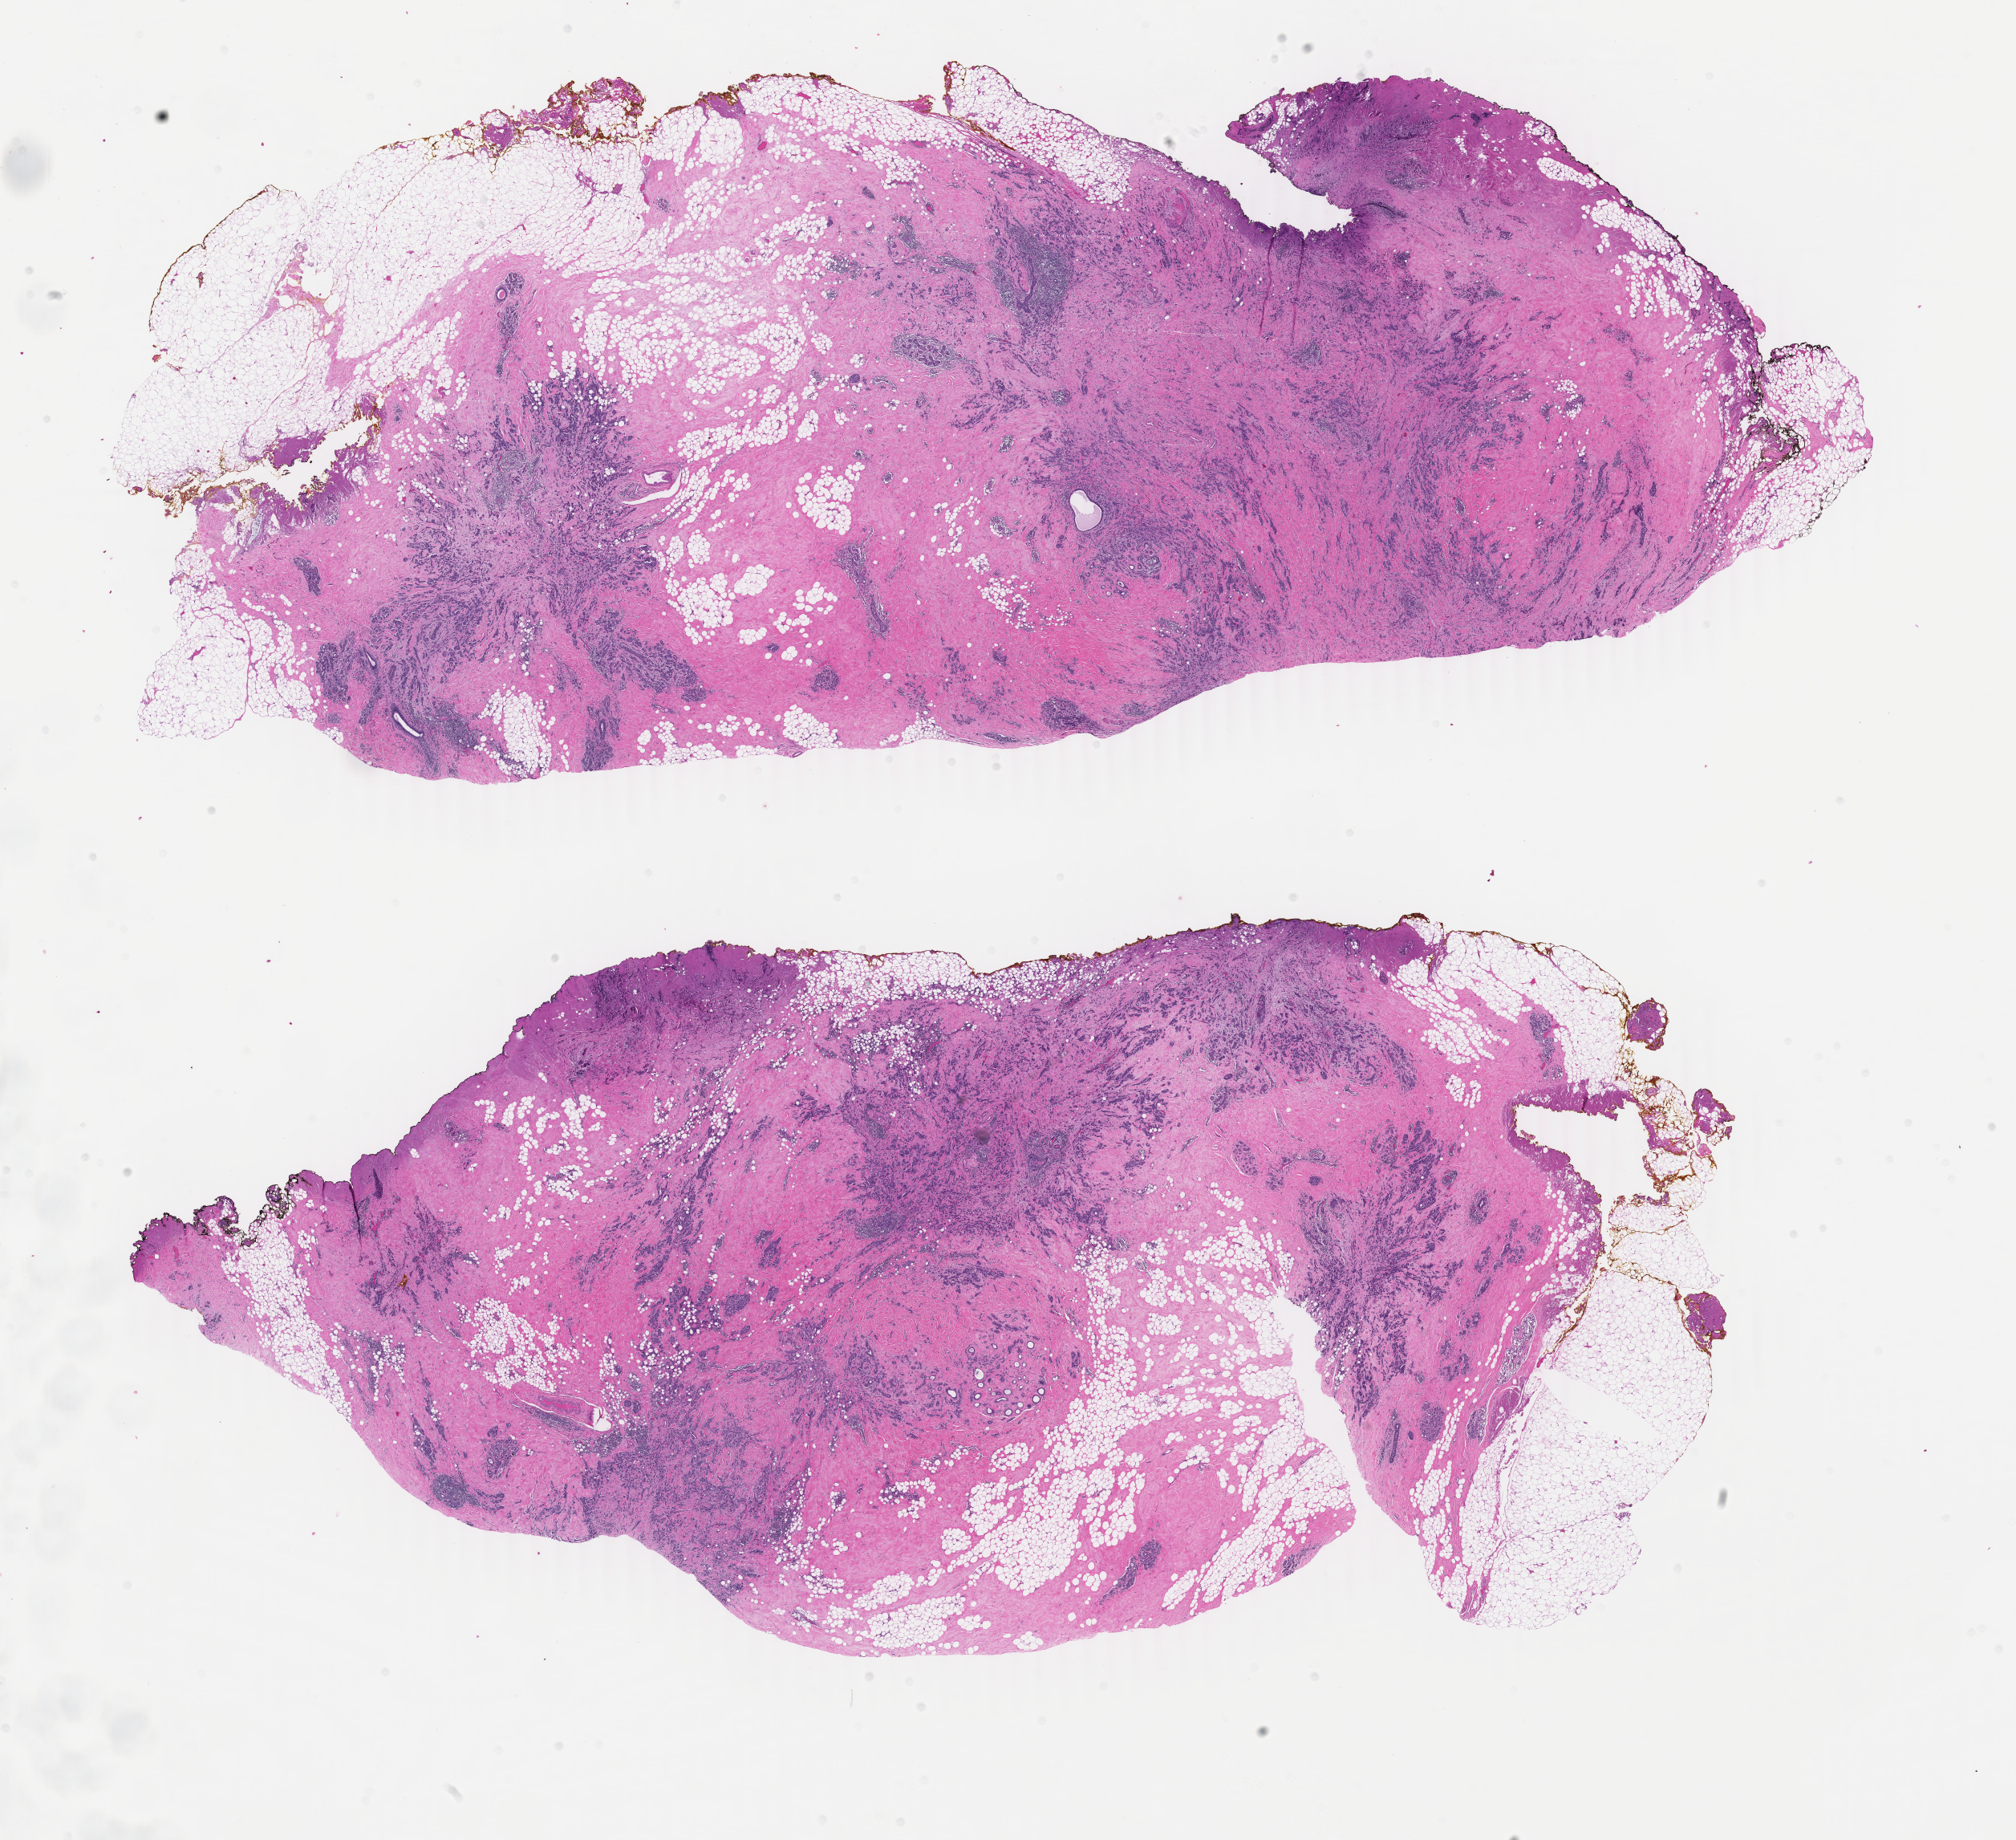
H&E-stained whole-slide image — low-resolution overview of the scanned area, about 20.0 x 18.2 mm, formalin-fixed paraffin-embedded (FFPE) diagnostic section, sample: primary tumour, breast. Female patient; age at initial diagnosis 46 years.
Histologic diagnosis: Lobular carcinoma, NOS. Laterality: left. AJCC pathologic stage: IIB (6th edition).